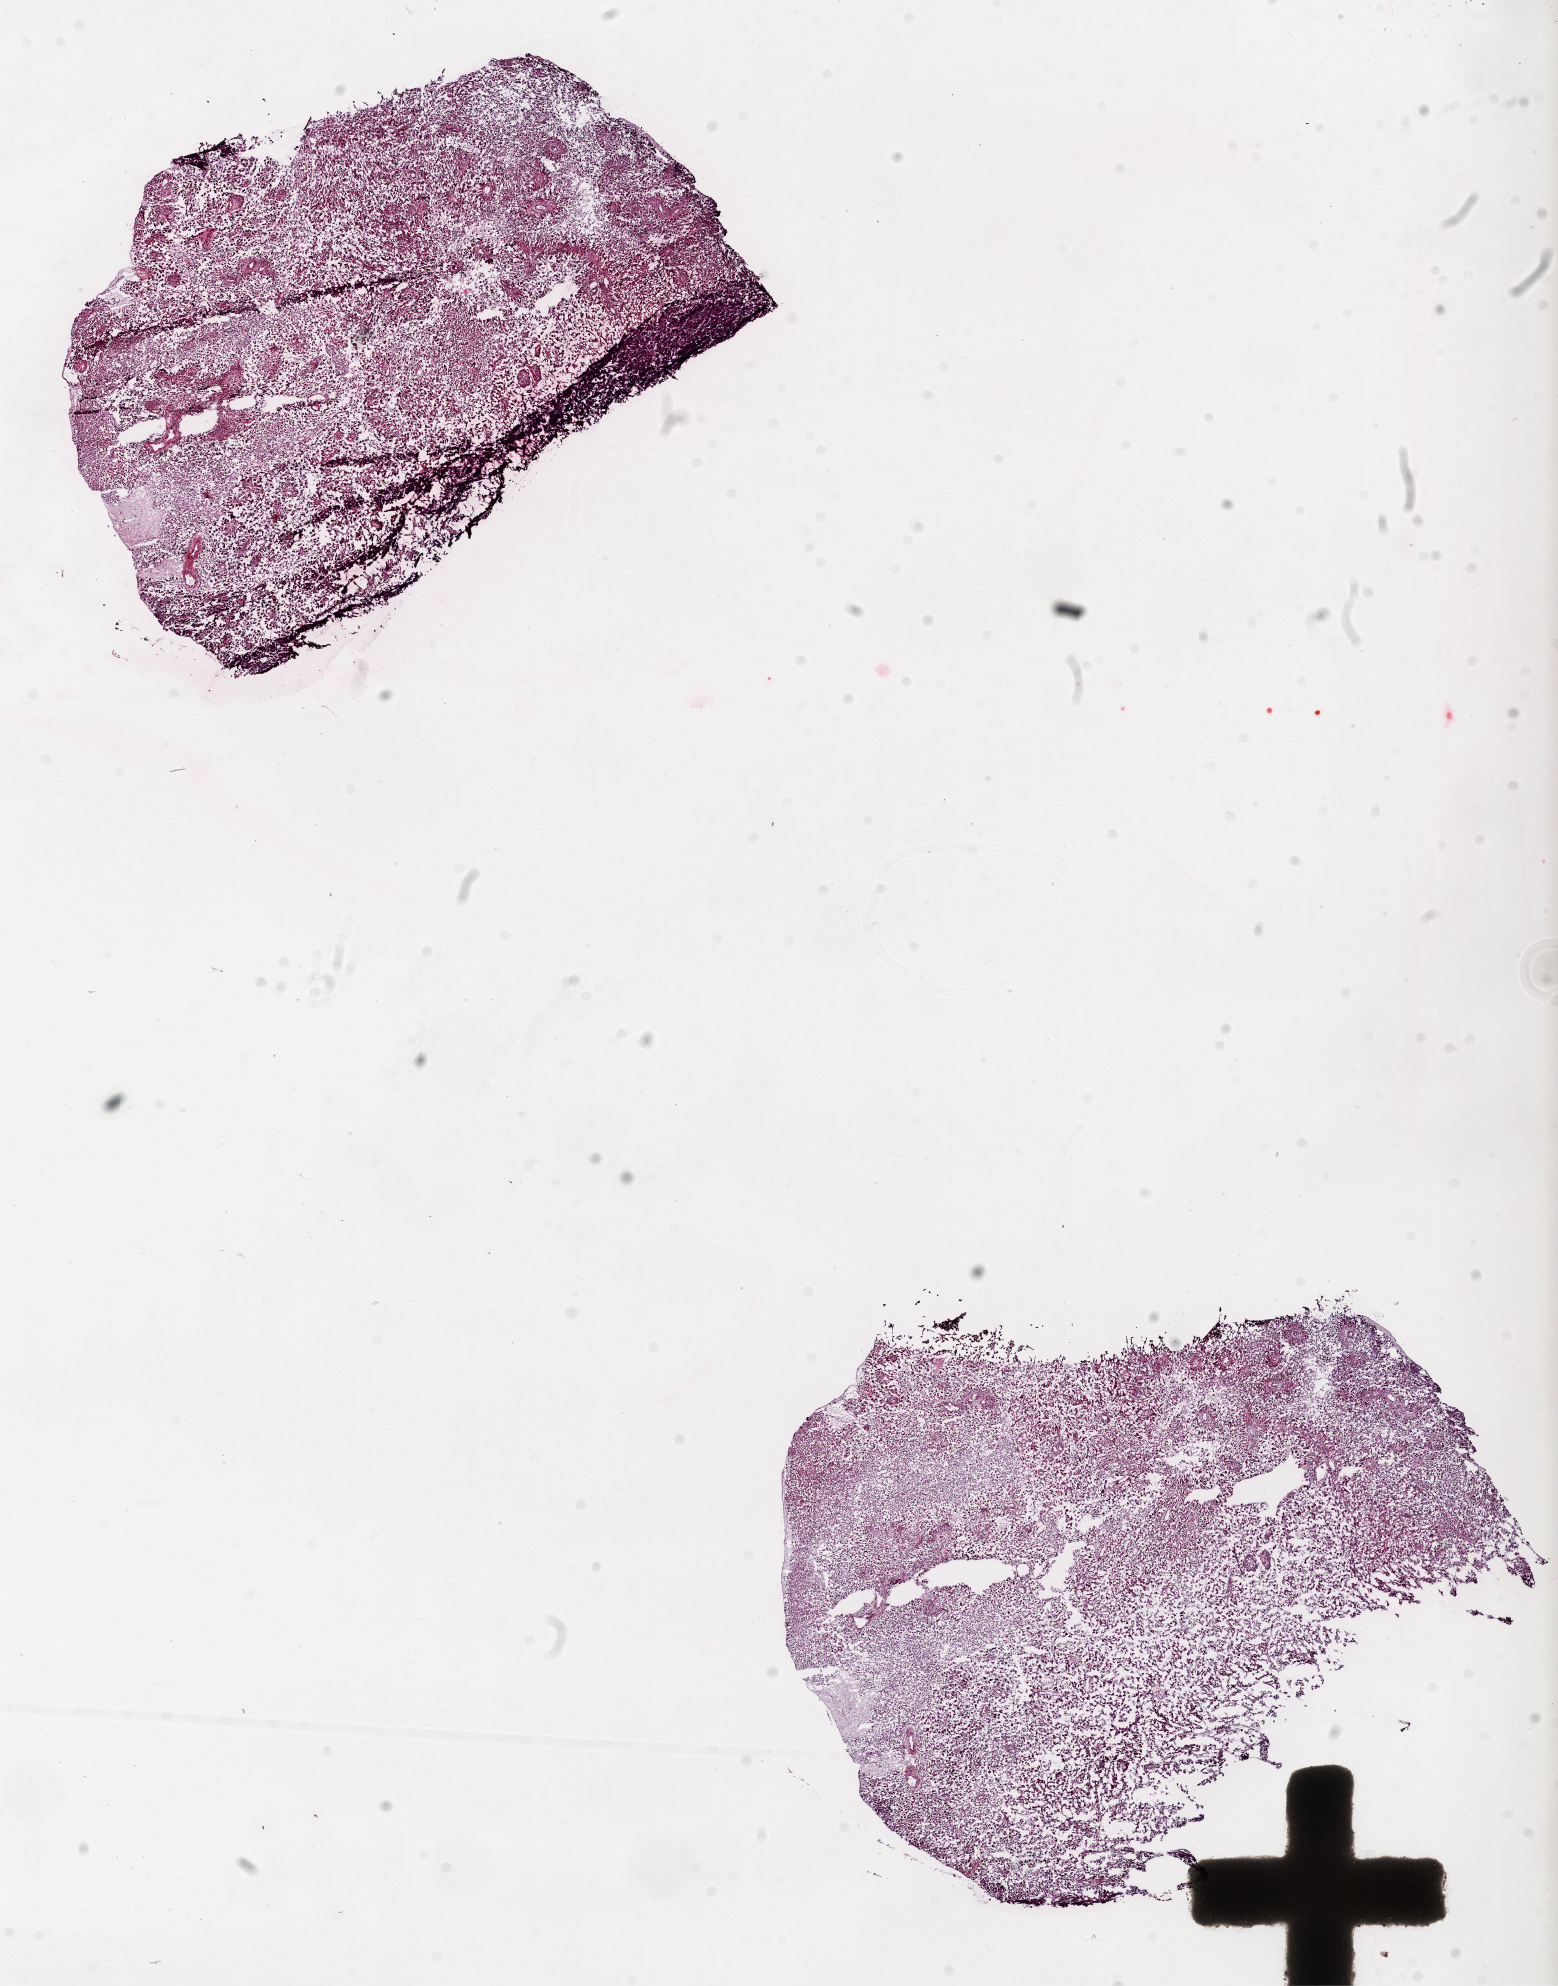
Whole-slide histology image, H&E-stained — low-resolution overview of the scanned area, about 12.6 x 16.0 mm (slide scanned at 20x). Frozen section. Brain, primary tumour sample. Patient: male, age at initial diagnosis 49 years. Composition of this section per pathologist review: tumour cells 90%, tumour nuclei 90%, necrosis 10%. Inflammatory infiltration, as recorded: monocyte infiltration 100%.
Diagnosis: Glioblastoma.